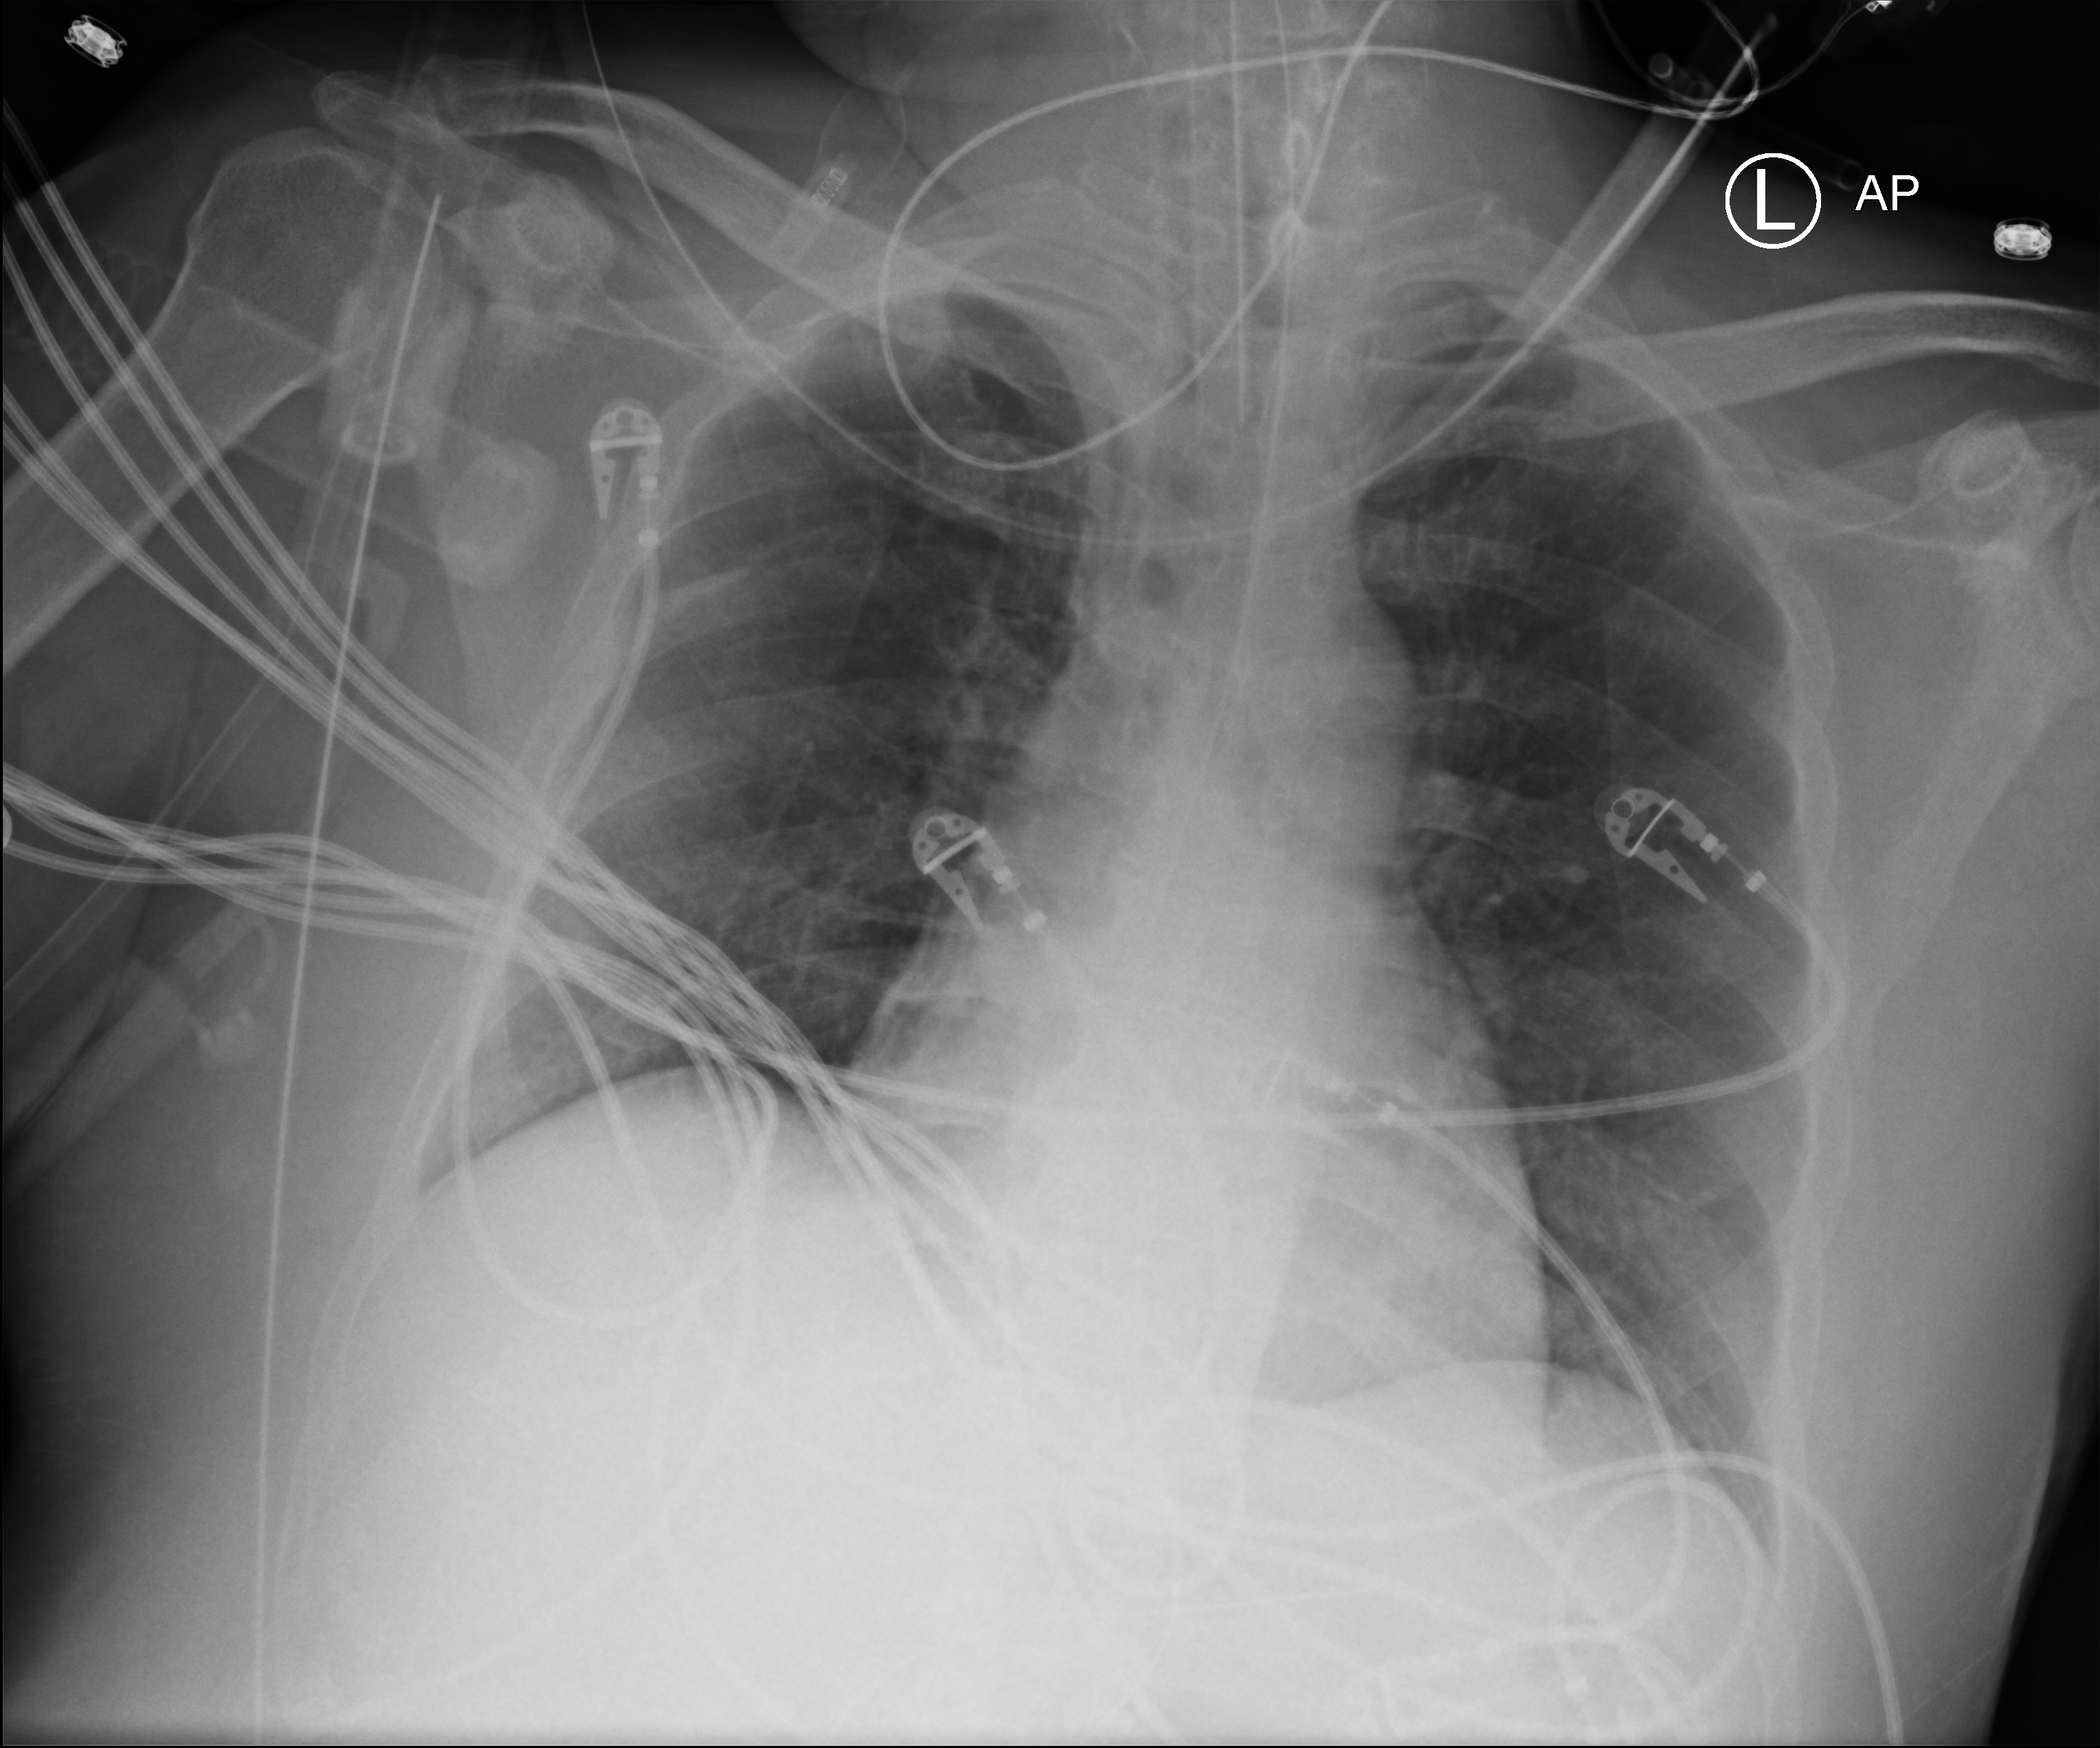
Chest X-ray (portable), anteroposterior (AP) projection. Patient hospitalised with COVID-19, aged 18–59 years.
From the hospital-stay record, not from the radiograph (when in the stay this image was taken is not recorded):
- hypertension (admission record): no